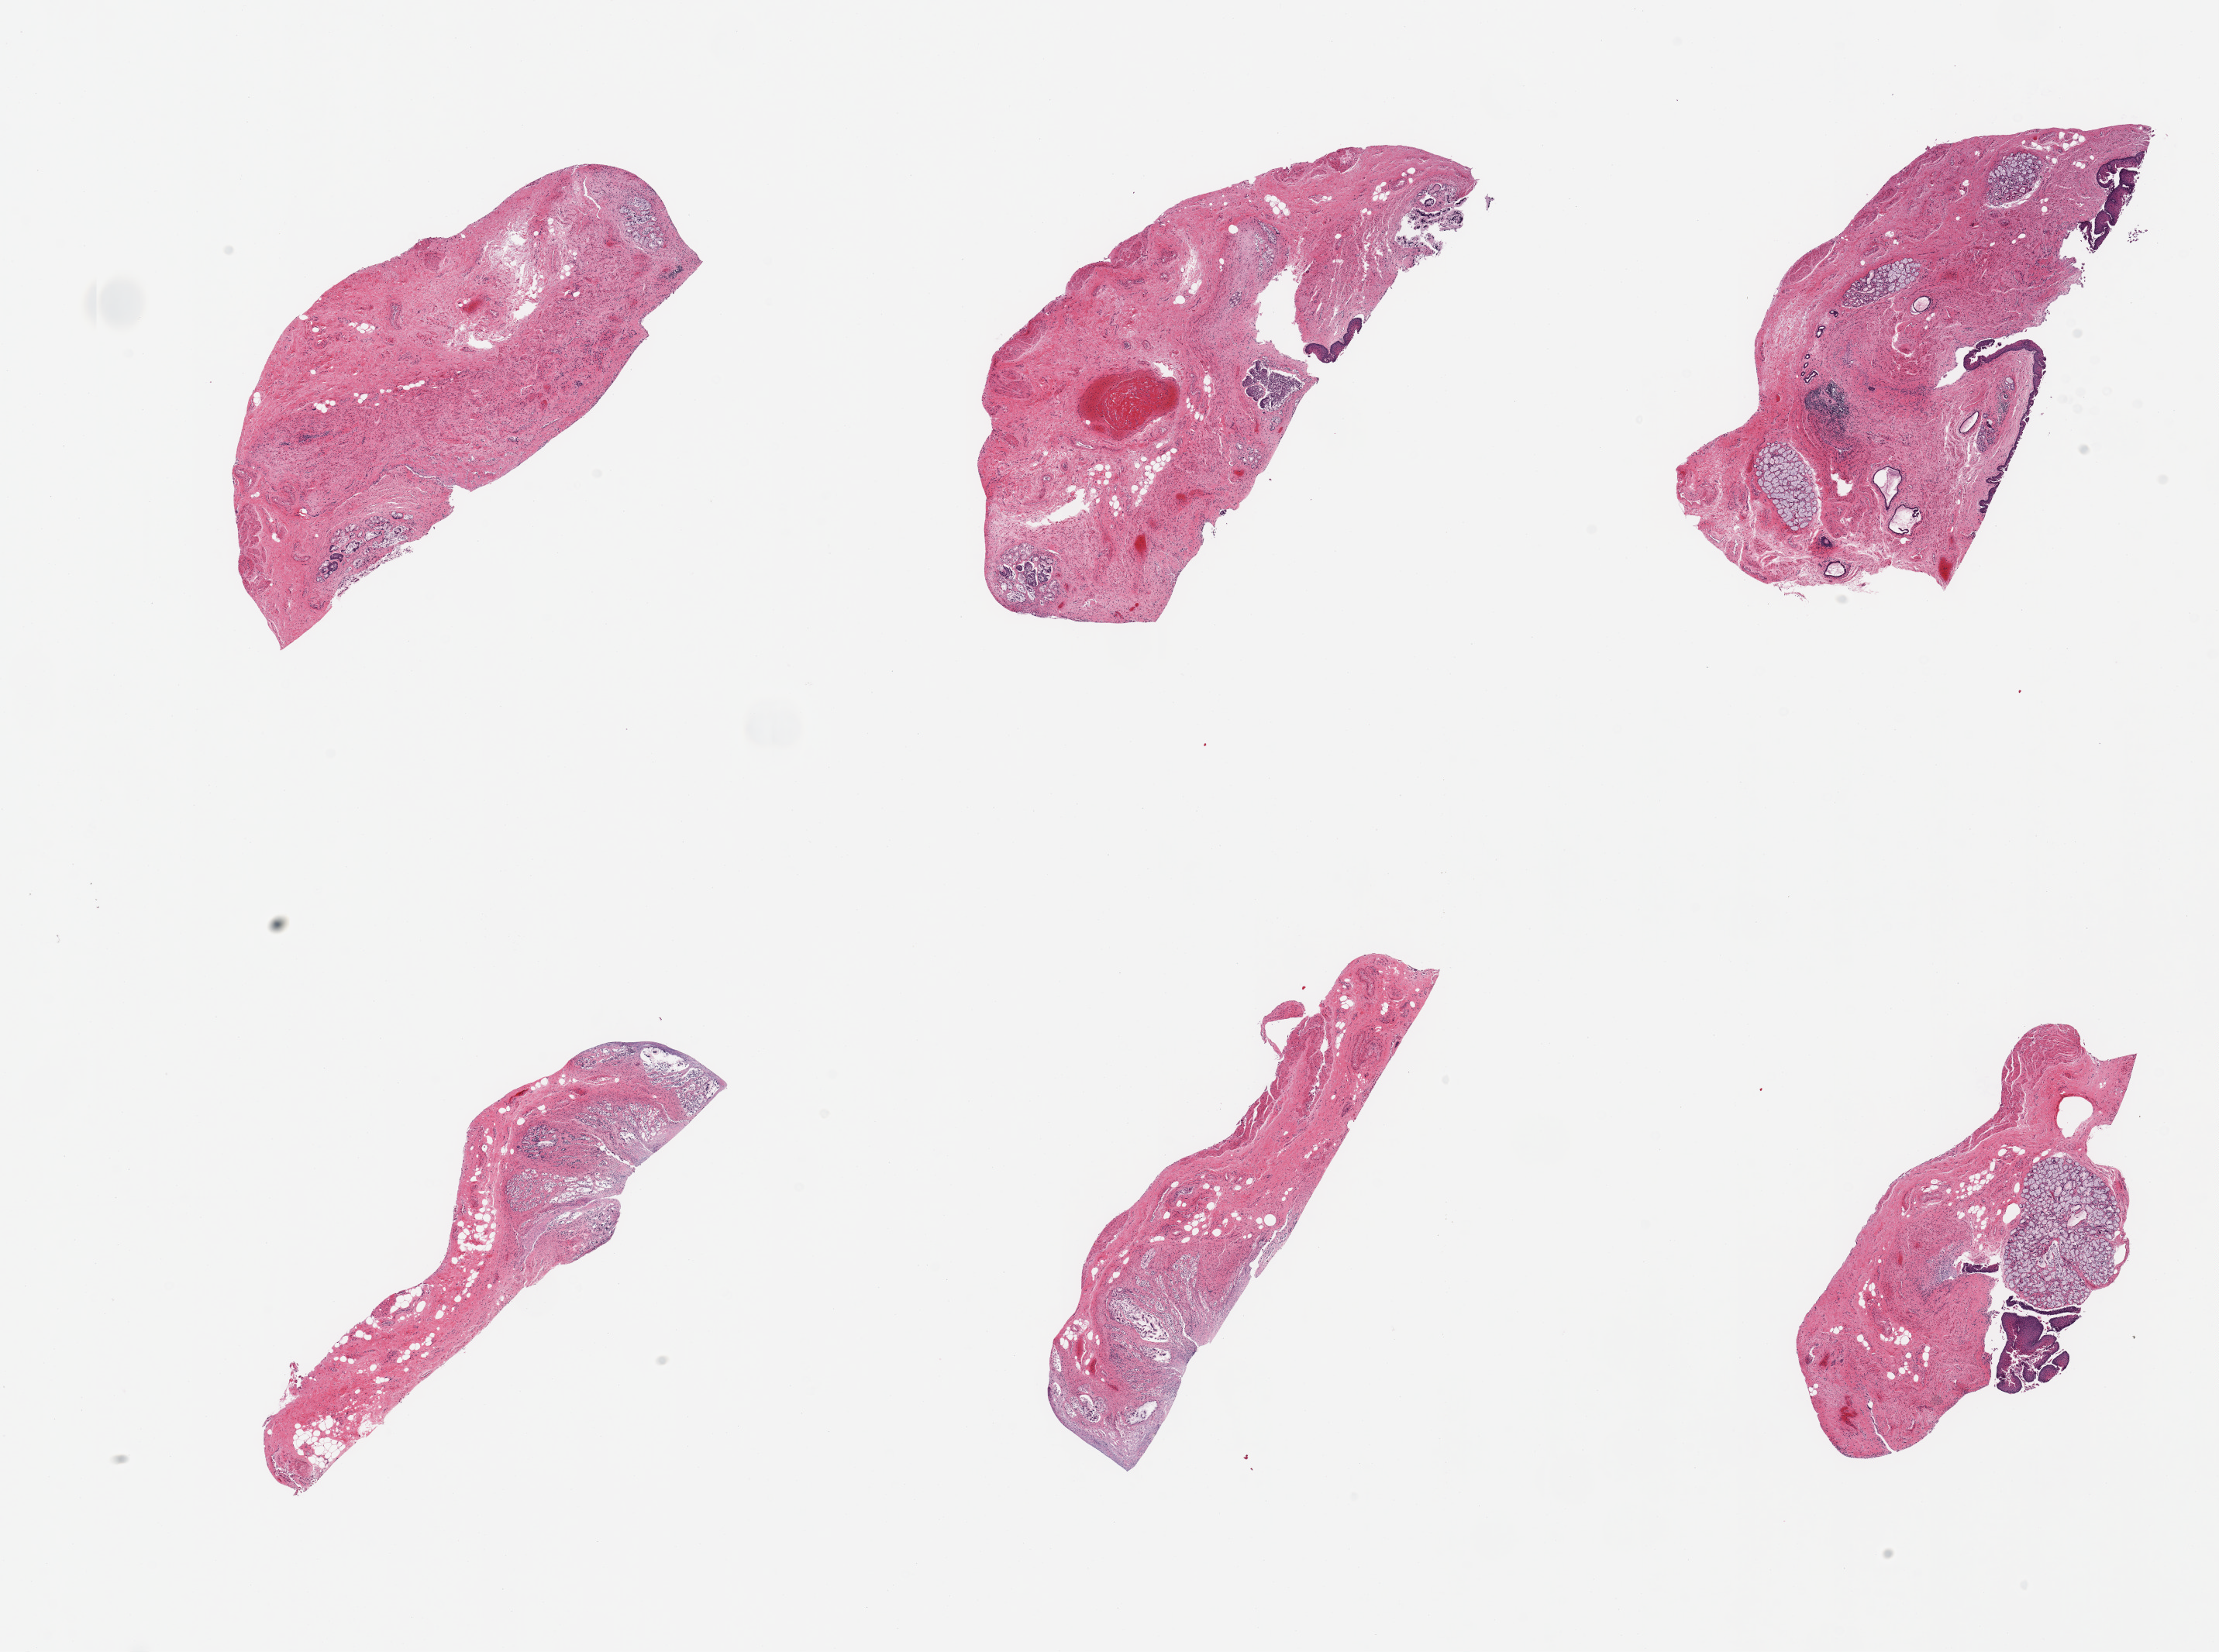
Digitized haematoxylin and eosin-stained section, a low-resolution overview of the entire scanned area, about 22.6 x 16.9 mm (acquisition: 20x scan). PAXgene-fixed paraffin-embedded (PFPE) section. Sampled site (target tissue): gastroesophageal junction. Tissue donor sample. Donor: female.
Reviewer comment on this tissue sample: 6 pieces; mucosa & submucosa with minimal muscularis.